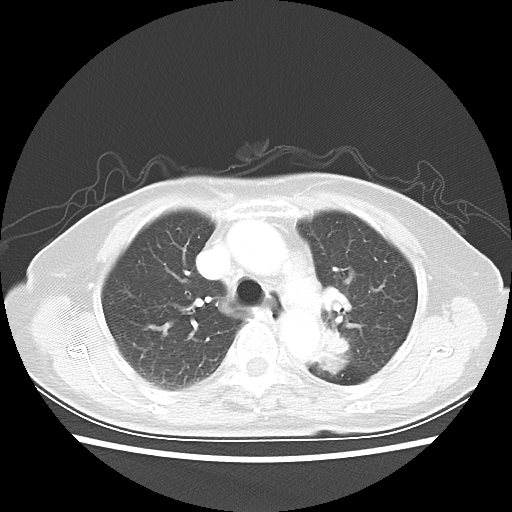
Chest CT, one axial slice; slice 34 of 50 in the series (ordered by position); lung window (W 1500 / L -600 HU); 5 mm slice thickness; 512 × 512 image matrix, field of view 335 × 335 mm. Female patient, age 81 years. Case-level facts recorded for this patient, not image findings: clinical TNM (as recorded): T2 N0 M1a.
Structures marked on this image (bounding box drawn by a radiologist):
- lung tumour (recorded histology: squamous cell carcinoma): bounding box <310,321,348,377> (left, top, right, bottom; pixels)